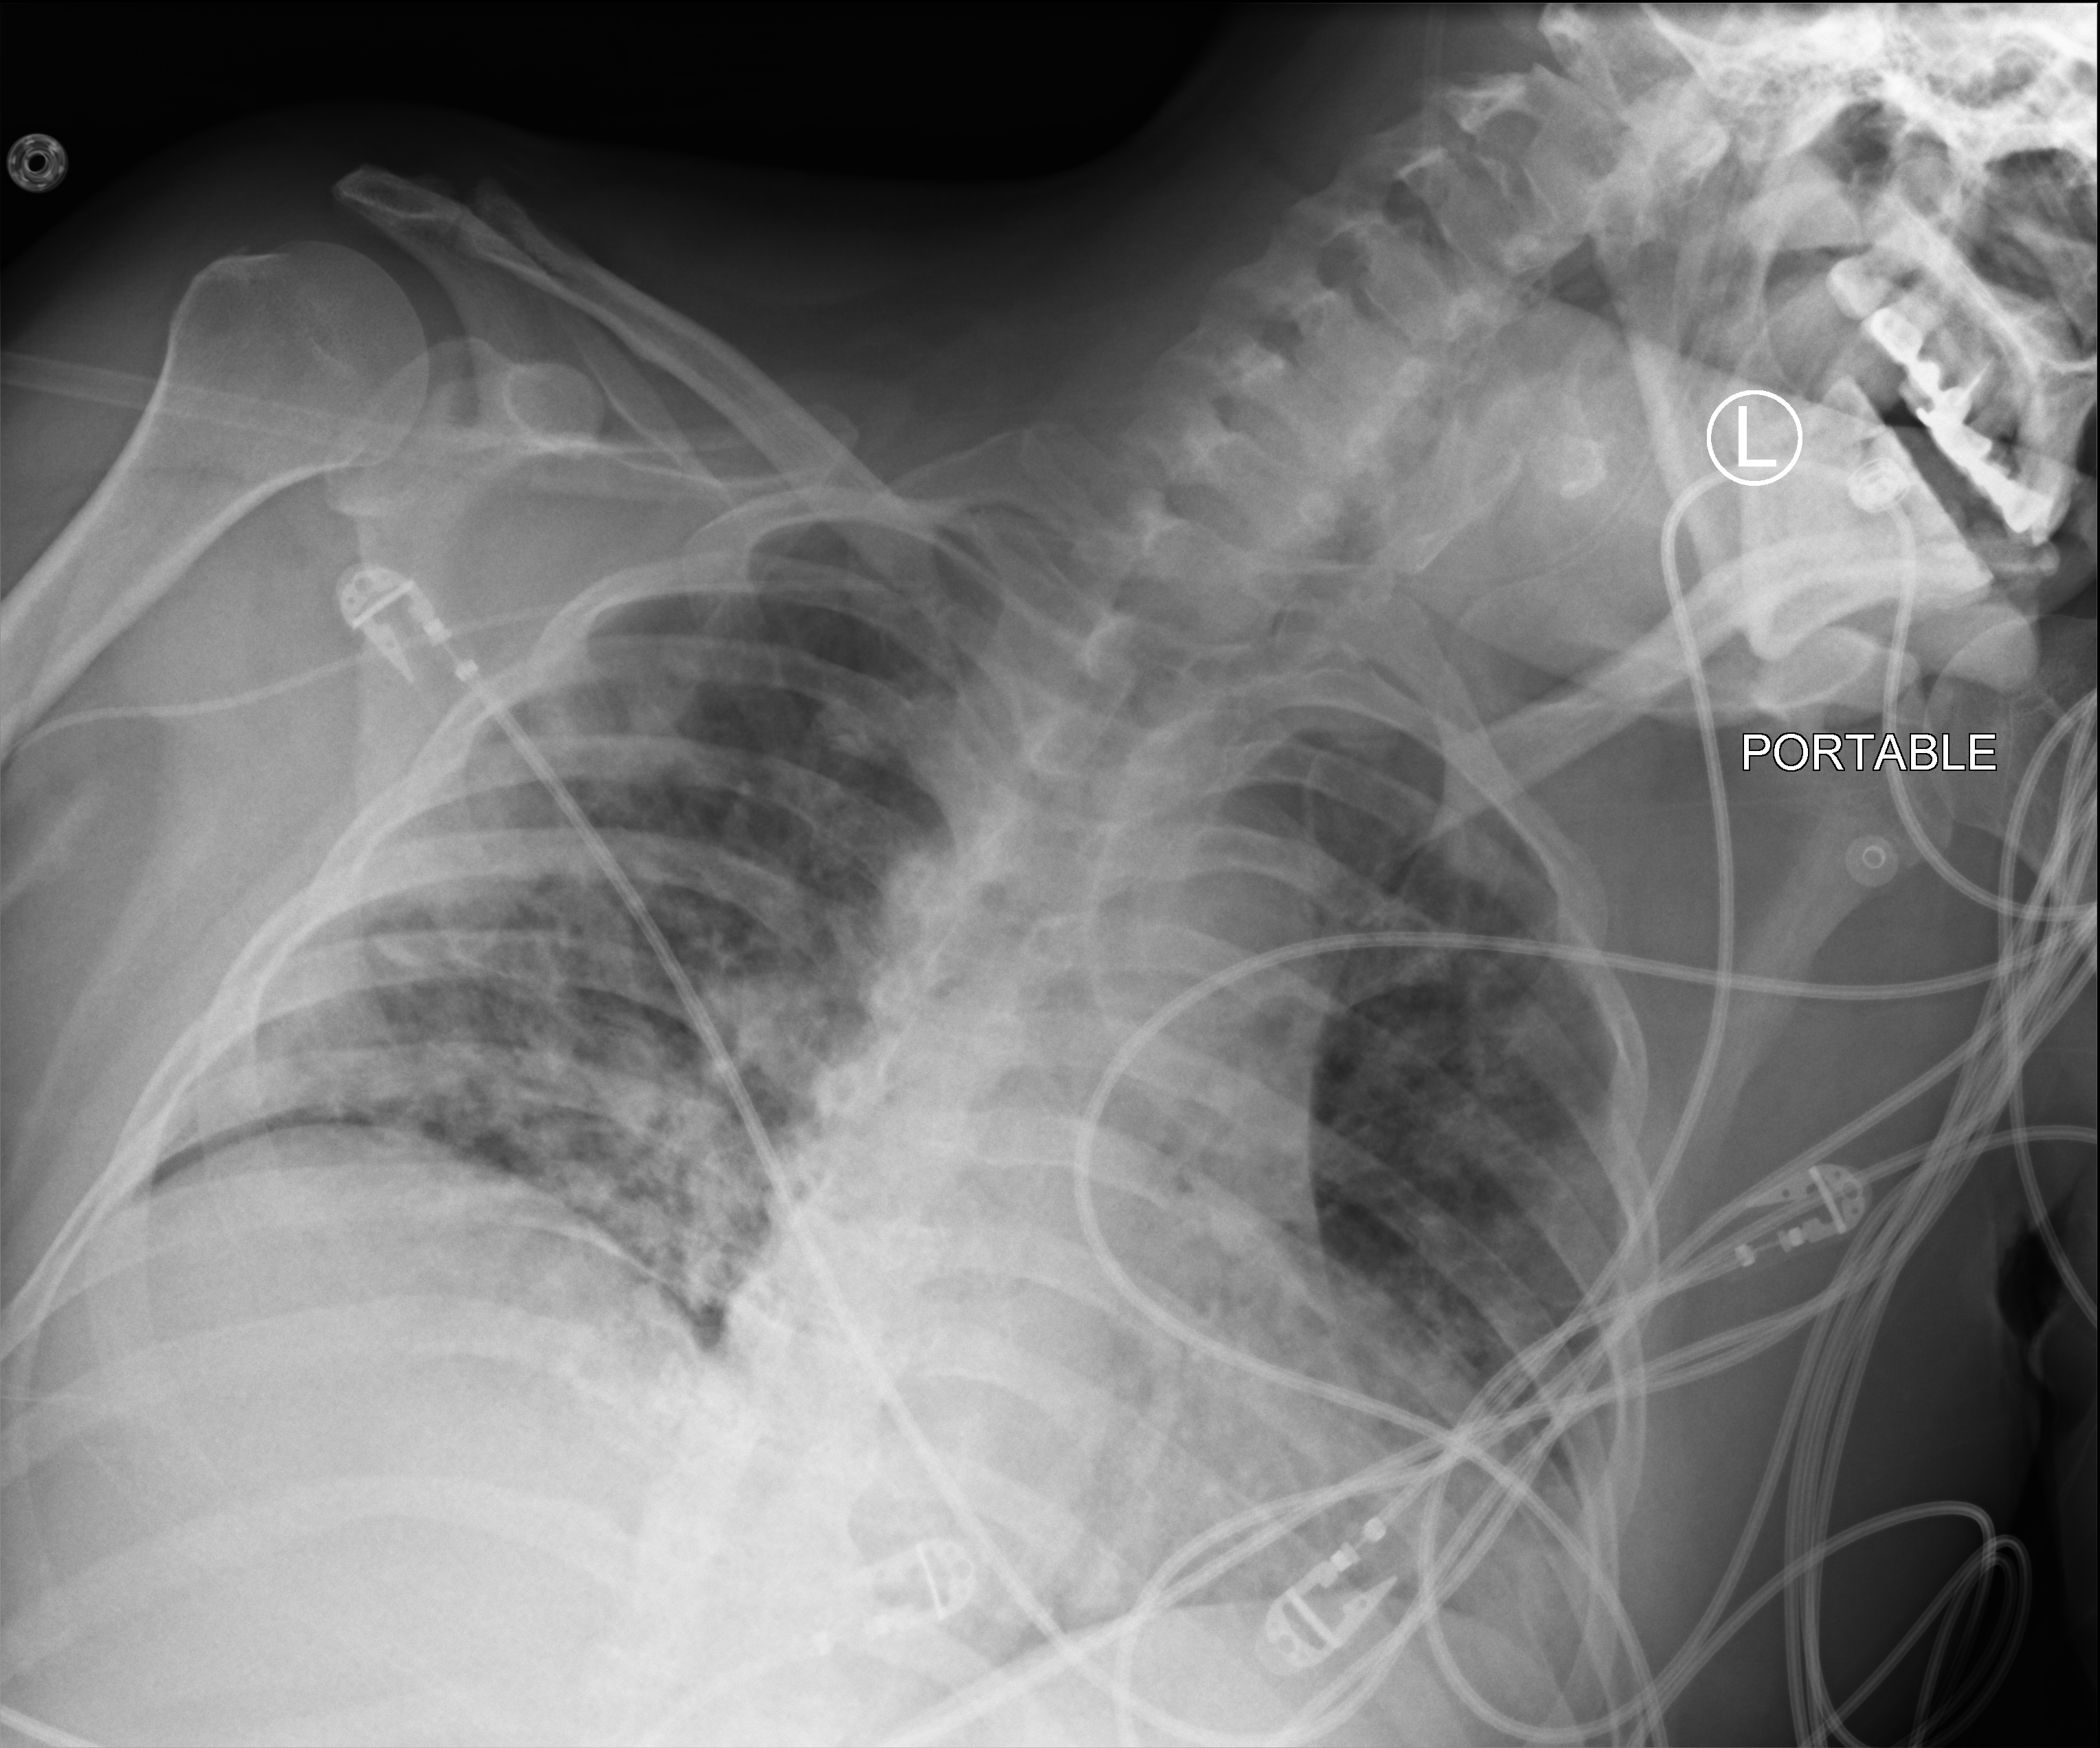
Portable chest radiograph; anteroposterior (AP) projection. Male patient hospitalised with COVID-19, age 18–59 years.
Admission-level facts for this patient (not findings on this image; timing relative to this image not recorded):
- mechanically ventilated during this hospital stay: yes